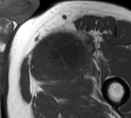
MRI of an extremity soft-tissue mass, one axial slice. Position 50 of 55 along the scan axis. MR volume resampled by the dataset authors to the PET/CT grid (not the native acquisition matrix). 131 × 118 image matrix, field of view 128 × 115 mm. Male patient. From the clinical record (not read from this slice): histological type: pleiomorphic liposarcoma; grade: high; site of the primary tumour: left thigh.
Annotated regions visible in this slice (expert contour drawn on MRI and transferred to this co-registered scan by the dataset authors):
- gross tumour volume including surrounding oedema: bounding box (x1, y1, x2, y2) in pixels: (32, 25, 97, 78)
- gross tumour volume (mass): (32, 34, 79, 72)